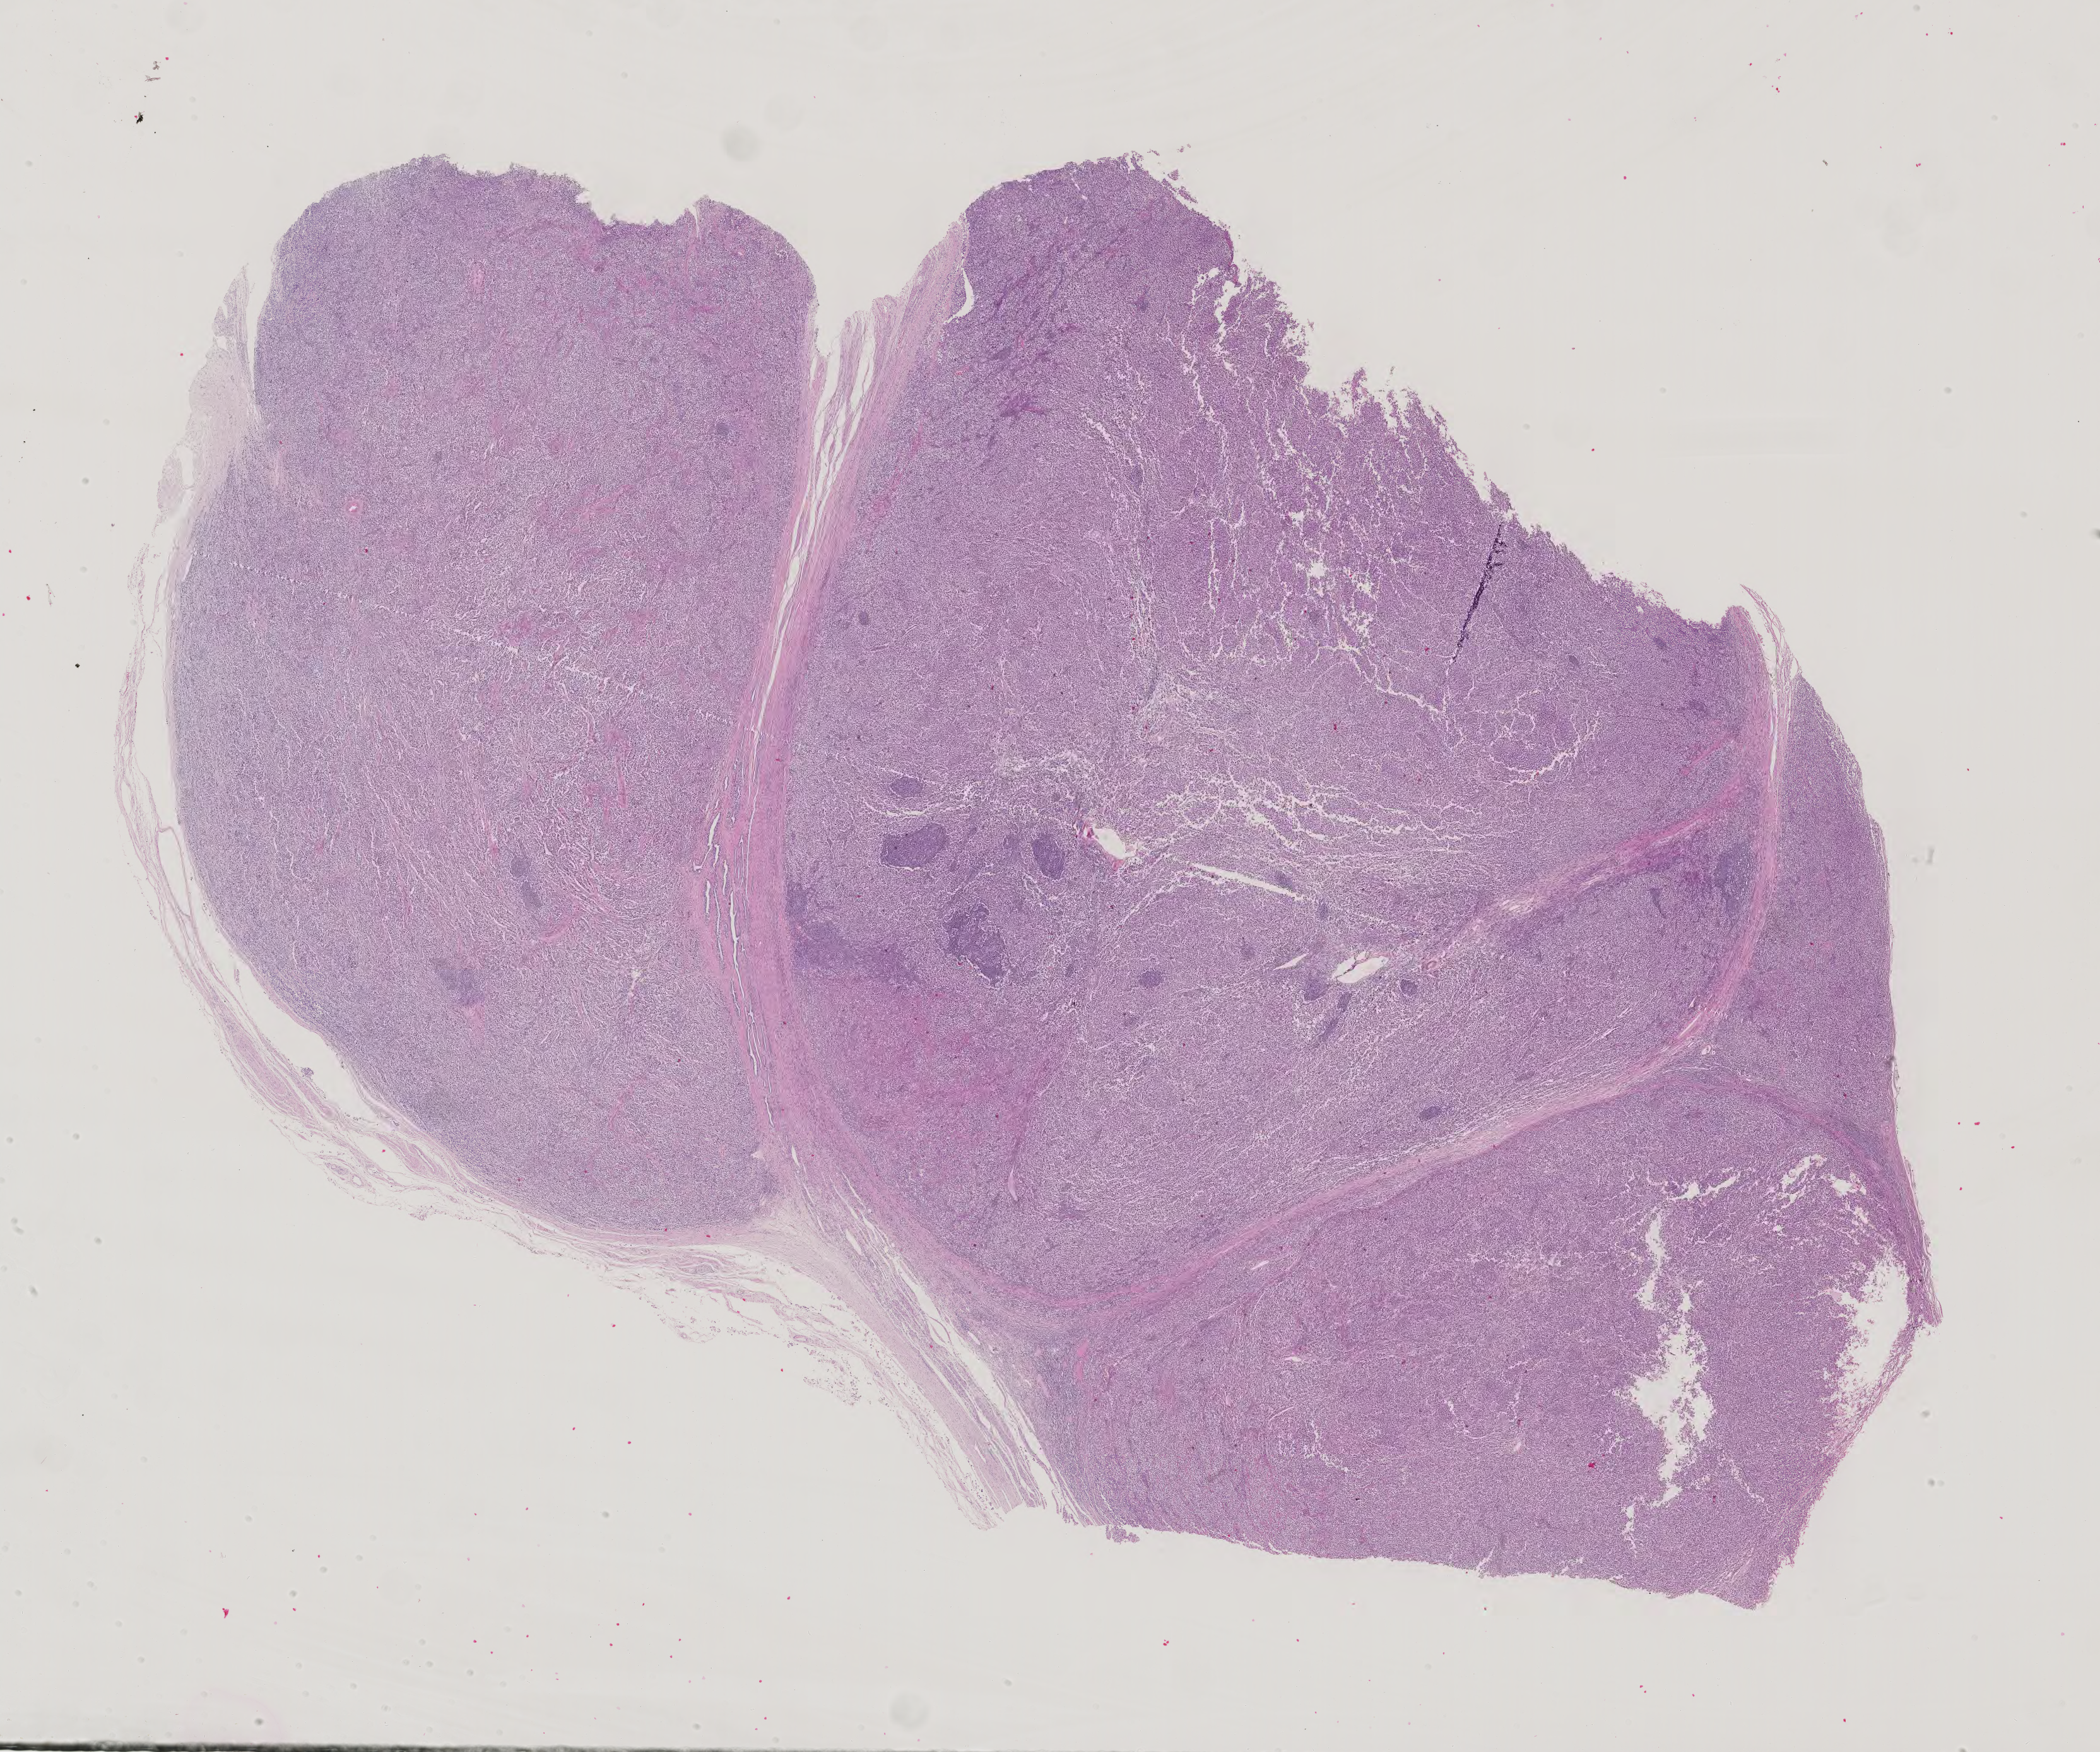
H&E whole-slide image, shown as a low-resolution overview of the whole scanned area (about 24.2 x 20.2 mm), formalin-fixed paraffin-embedded (FFPE) diagnostic section, testis, additional new primary tumour sample. Male, age 22 years at initial diagnosis.
This section: additional new primary tumour. Patient diagnosis: Embryonal carcinoma, NOS.